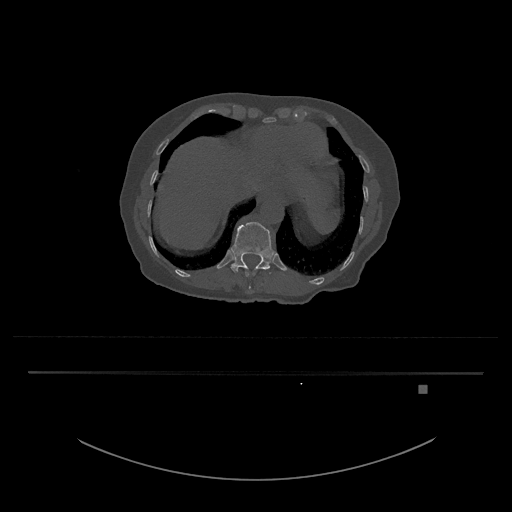
CT including the spine, one axial slice. Slice 629 of 797 in the series (ordered by position). 120 kVp. Bone window (W 1800 / L 400 HU). 0.5 mm slice thickness. 512 × 512 image matrix, field of view 500 × 500 mm. Patient: female, 57 years. Case-level facts recorded for this patient, not image findings: primary cancer: cervical.
Structures marked on this image (semi-automatically segmented with operator editing):
- T11 vertebra: bounding box (x1, y1, x2, y2) in pixels: (245, 268, 260, 290)
- T12 vertebra: (231, 222, 274, 273)